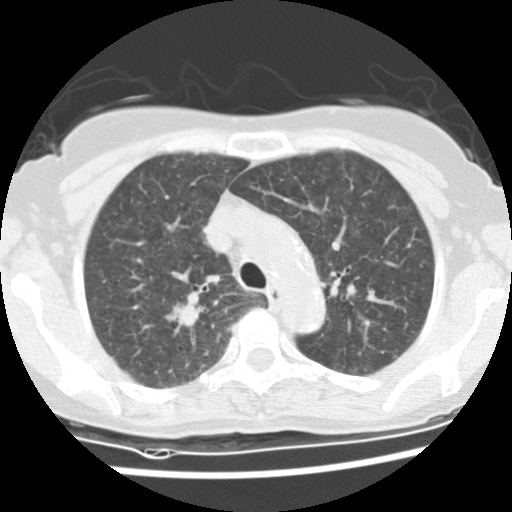
Chest CT (low-dose screening protocol), one axial image; baseline annual screen; lung window (W 1500 / L -600 HU); 2.5 mm slice thickness; standard (soft-tissue) reconstruction kernel (STANDARD); 120 kVp; 512 × 512 image matrix, field of view 298 × 298 mm. Female, age 66 years at enrolment. Current smoker at enrolment.
Expert-annotated lung lesion, bounding box [x1, y1, x2, y2] px = [149, 289, 202, 334]. The exam's reader record, not a measurement of the box and not confirmed to be the same lesion: non-calcified nodule or mass ≥4 mm, right upper lobe, 13 × 11 mm, soft tissue attenuation. Official screen result: positive, change unspecified: nodule(s) >= 4 mm or enlarging nodule(s), mass(es), or other non-specific abnormalities suspicious for lung cancer. Later outcome: lung cancer diagnosed 64 days after this screen — adenocarcinoma, NOS, right upper lobe, poorly differentiated (G3), stage IA (AJCC 6th edition), 18 mm at pathology.